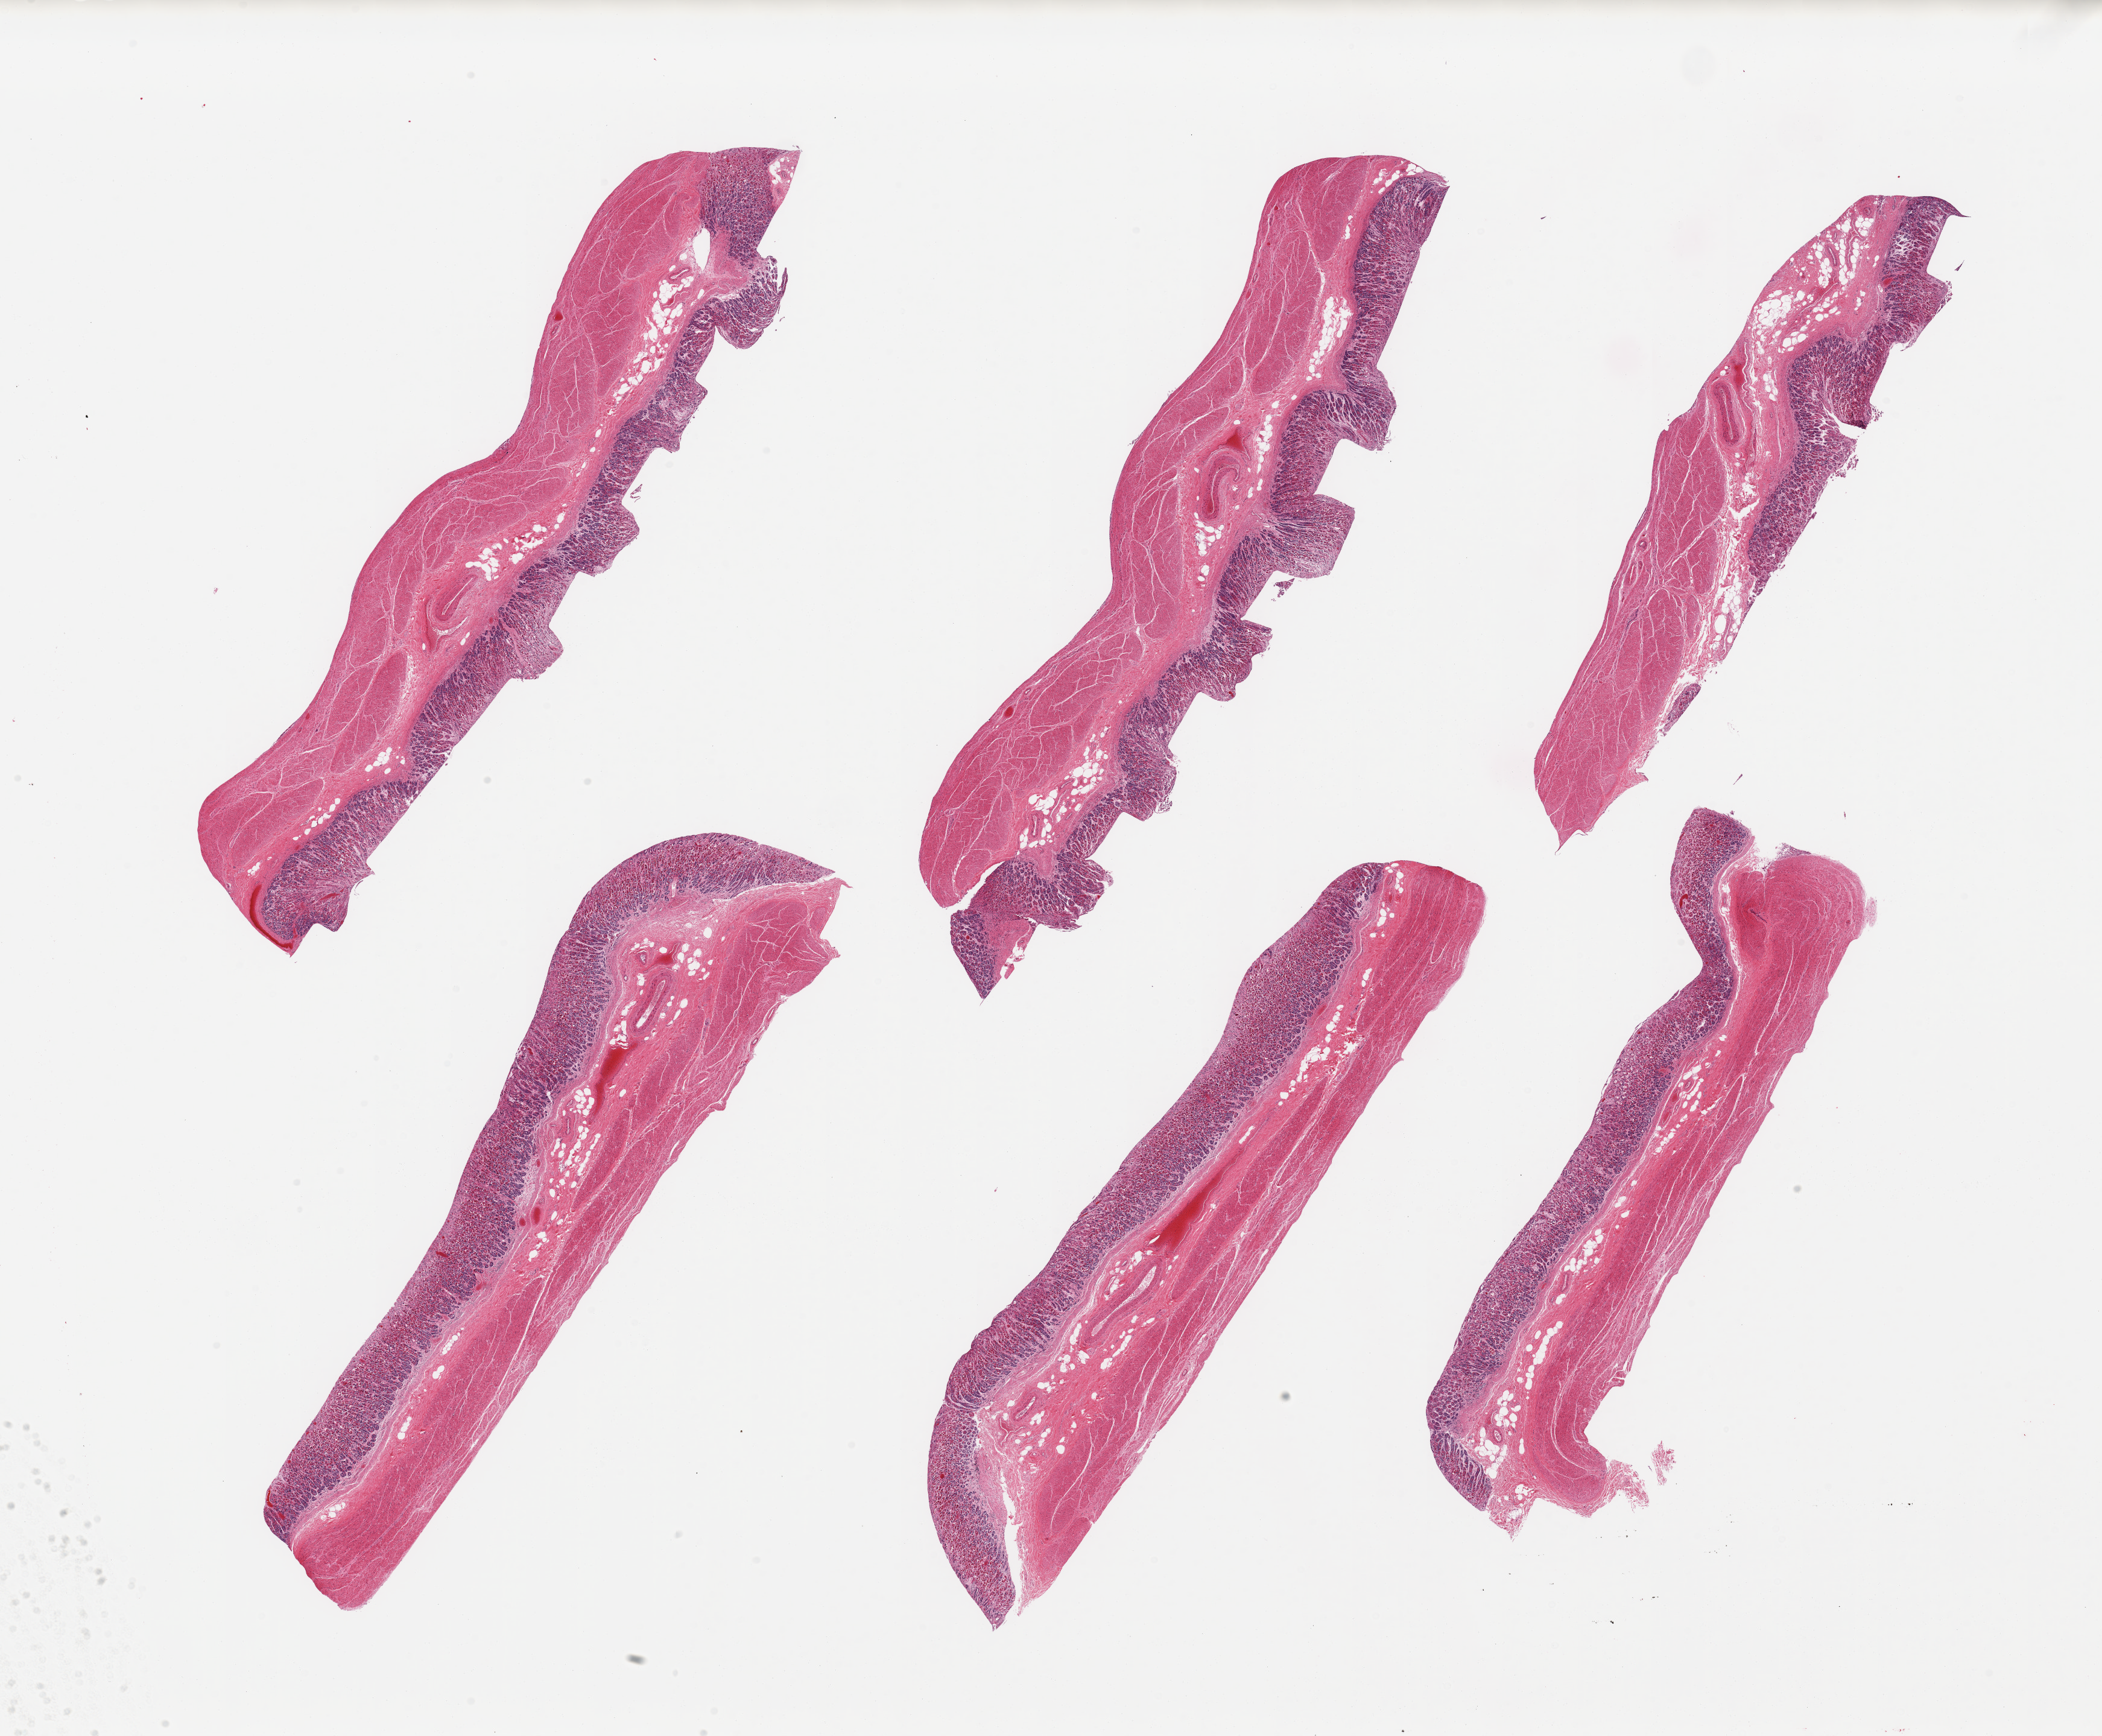
Digitized H&E-stained section — a low-resolution overview of the entire scanned area, about 27.6 x 22.8 mm (acquisition: 20x scan). PAXgene-fixed paraffin-embedded (PFPE) section. Section of stomach (target tissue). Tissue donor sample. Donor sex: male.
Pathologist's review note for this sample: 6 pieces; mildly autolyzed gastric mucosa and preserved muscularis.